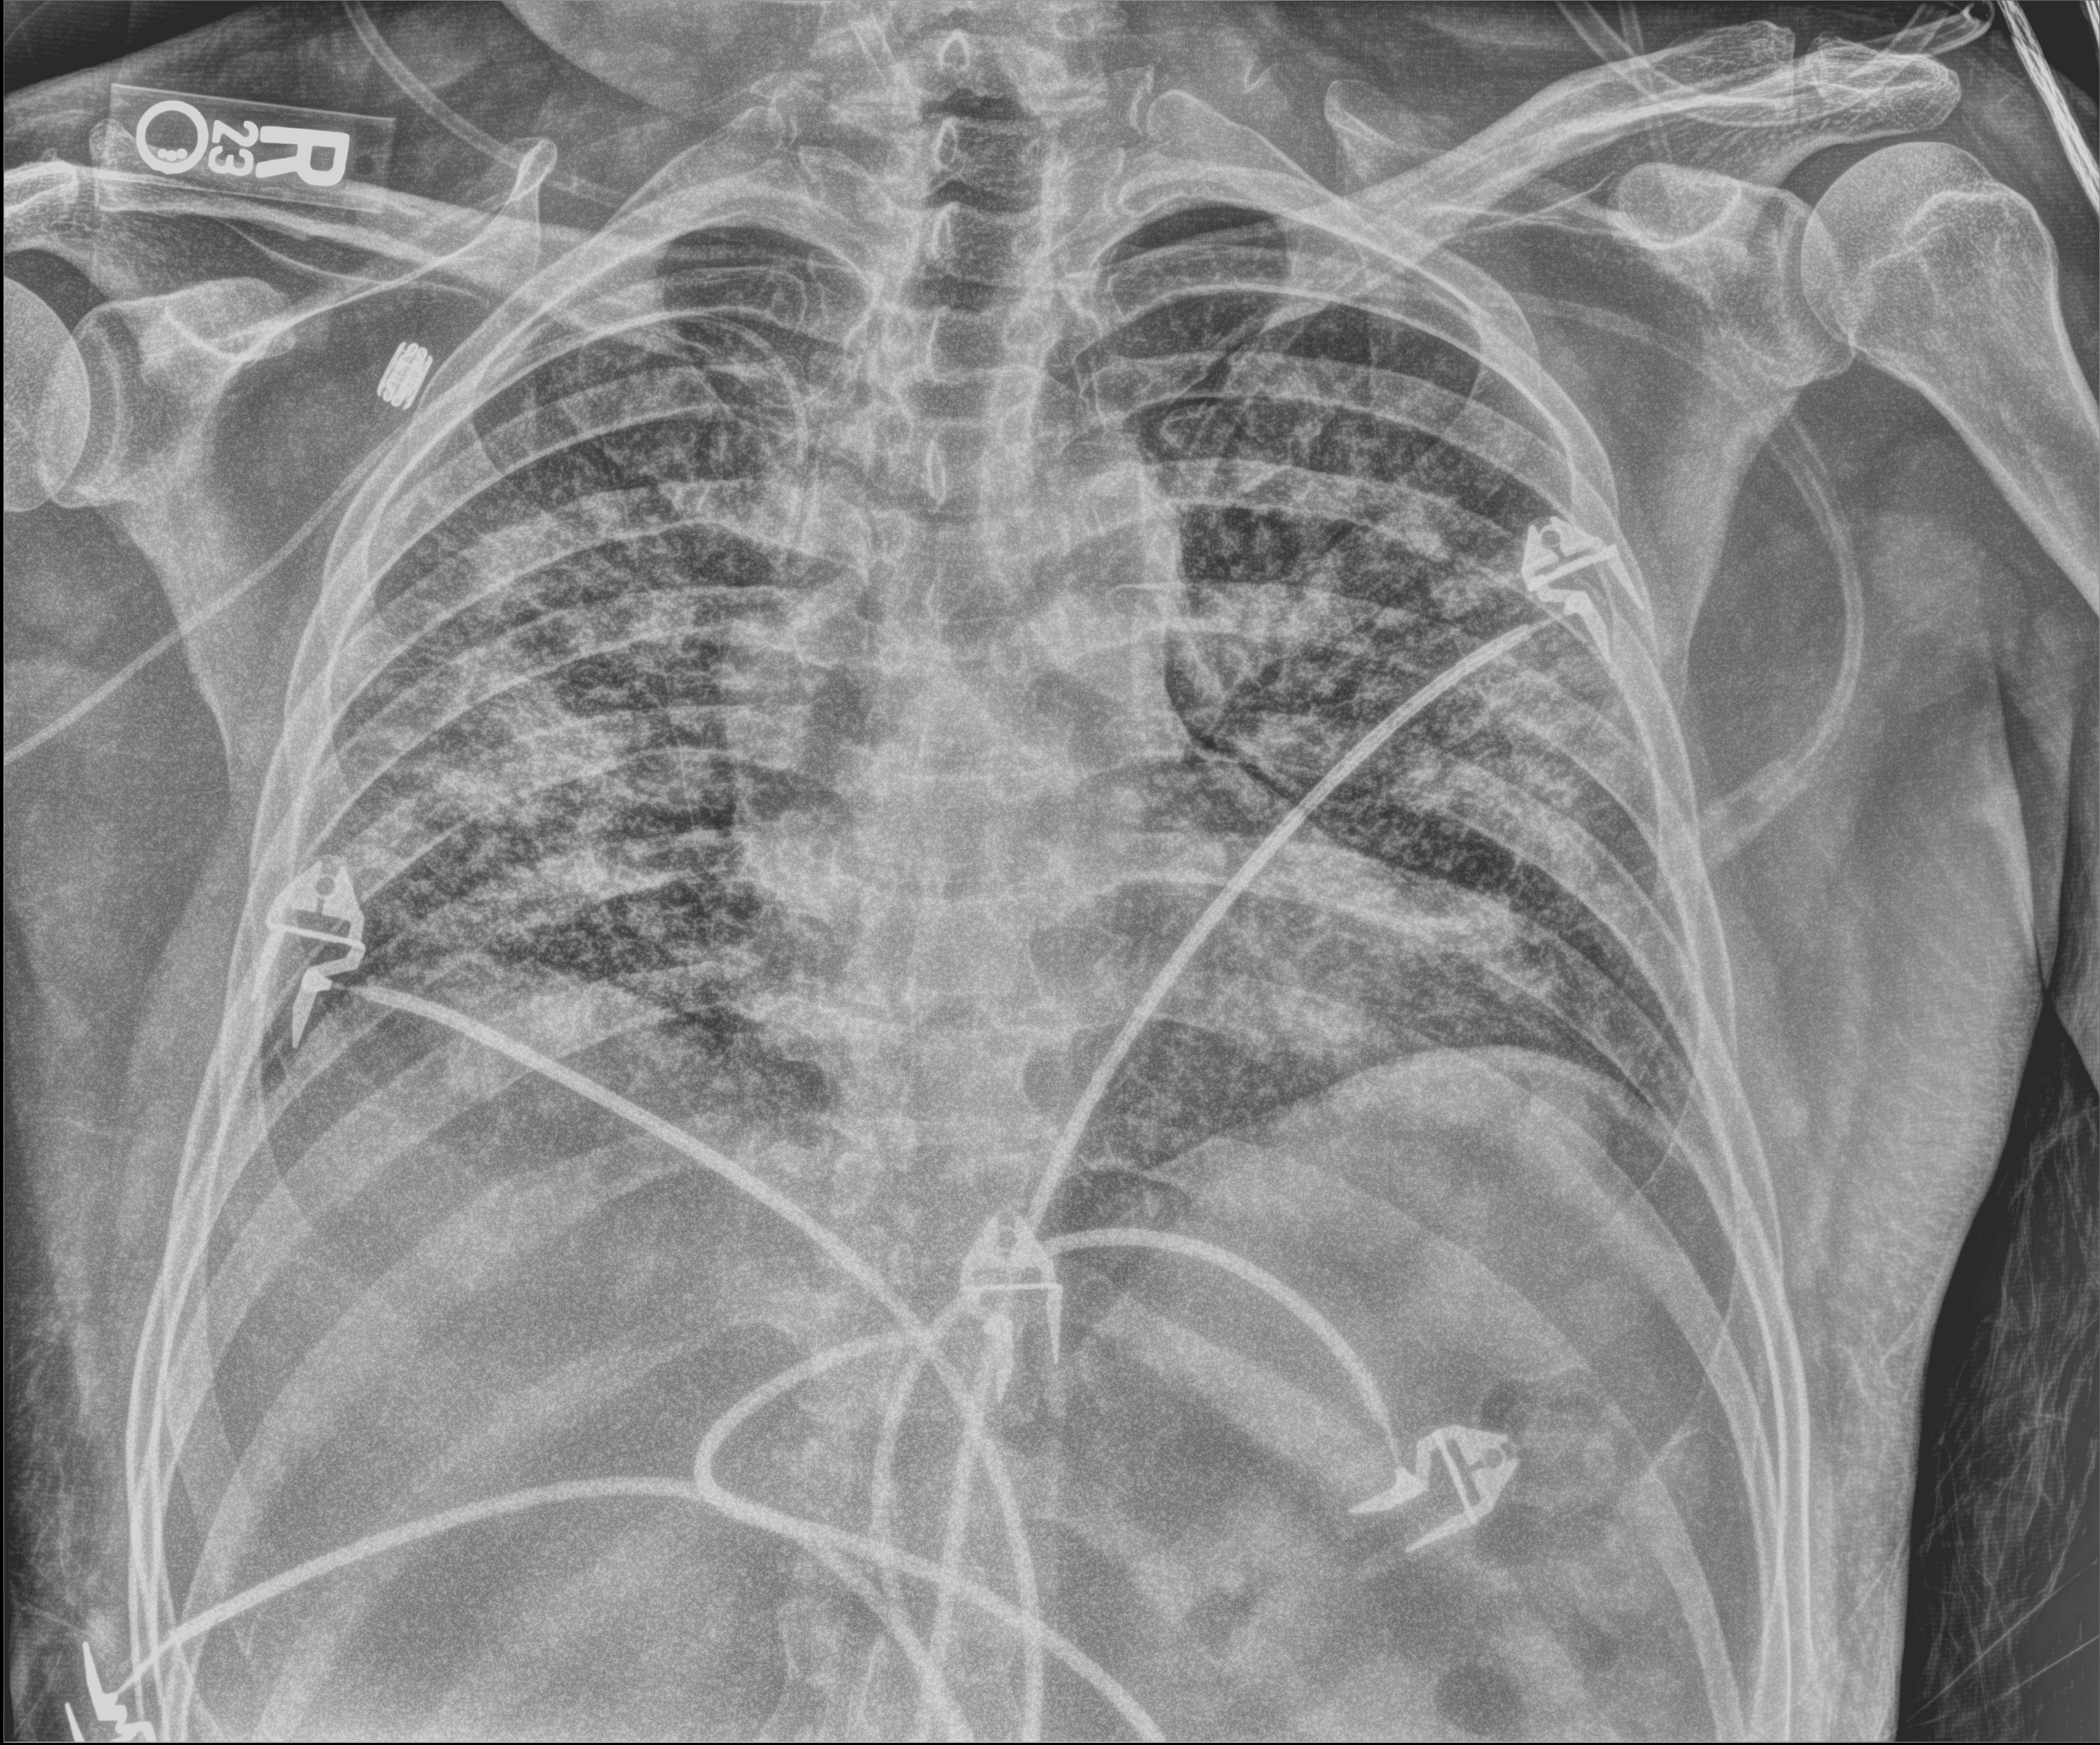
Chest radiograph, anteroposterior (AP) projection. Male patient hospitalised with COVID-19, age 18–59 years.
From the hospital-stay record, not from the radiograph (when in the stay this image was taken is not recorded): length of hospital stay: 77 days.